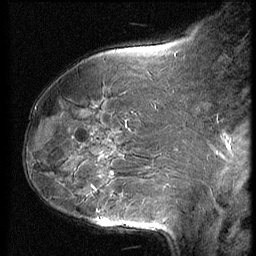
Breast MRI (dynamic contrast-enhanced), one sagittal slice. Slice 23 of 62 in the series (ordered by position). 3 images stored at this slice position (order not interpretable as contrast timing). 1.5 T. TE 4.2 ms, TR 9 ms. 2.5 mm slice thickness. 256 × 256 image matrix, field of view 180 × 180 mm. Patient: female, 50 years. From the clinical record (not read from this slice): setting: breast cancer imaged before/during neoadjuvant chemotherapy; receptor status: HR-positive, HER2-negative.
Outlined on this slice (semi-automatically segmented with operator editing):
- analysis volume of interest (the breast-tissue region the enhancement analysis was run in; not a lesion): bounding box [x1, y1, x2, y2] px = [59, 125, 139, 234]
- tumour enhancement mask (voxels above the 140 % enhancement threshold inside the analysis volume of interest): [98, 210, 108, 222]